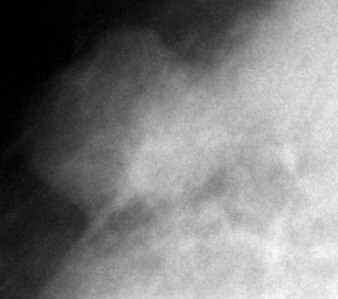
Region of interest cut from a scanned film mammogram (one marked finding); right breast; CC view; BI-RADS breast density category 3 (scale 1–4).
Marked abnormality: mass, shape oval, margins circumscribed; BI-RADS assessment category 4; pathology result (as recorded, not read from the image): benign.